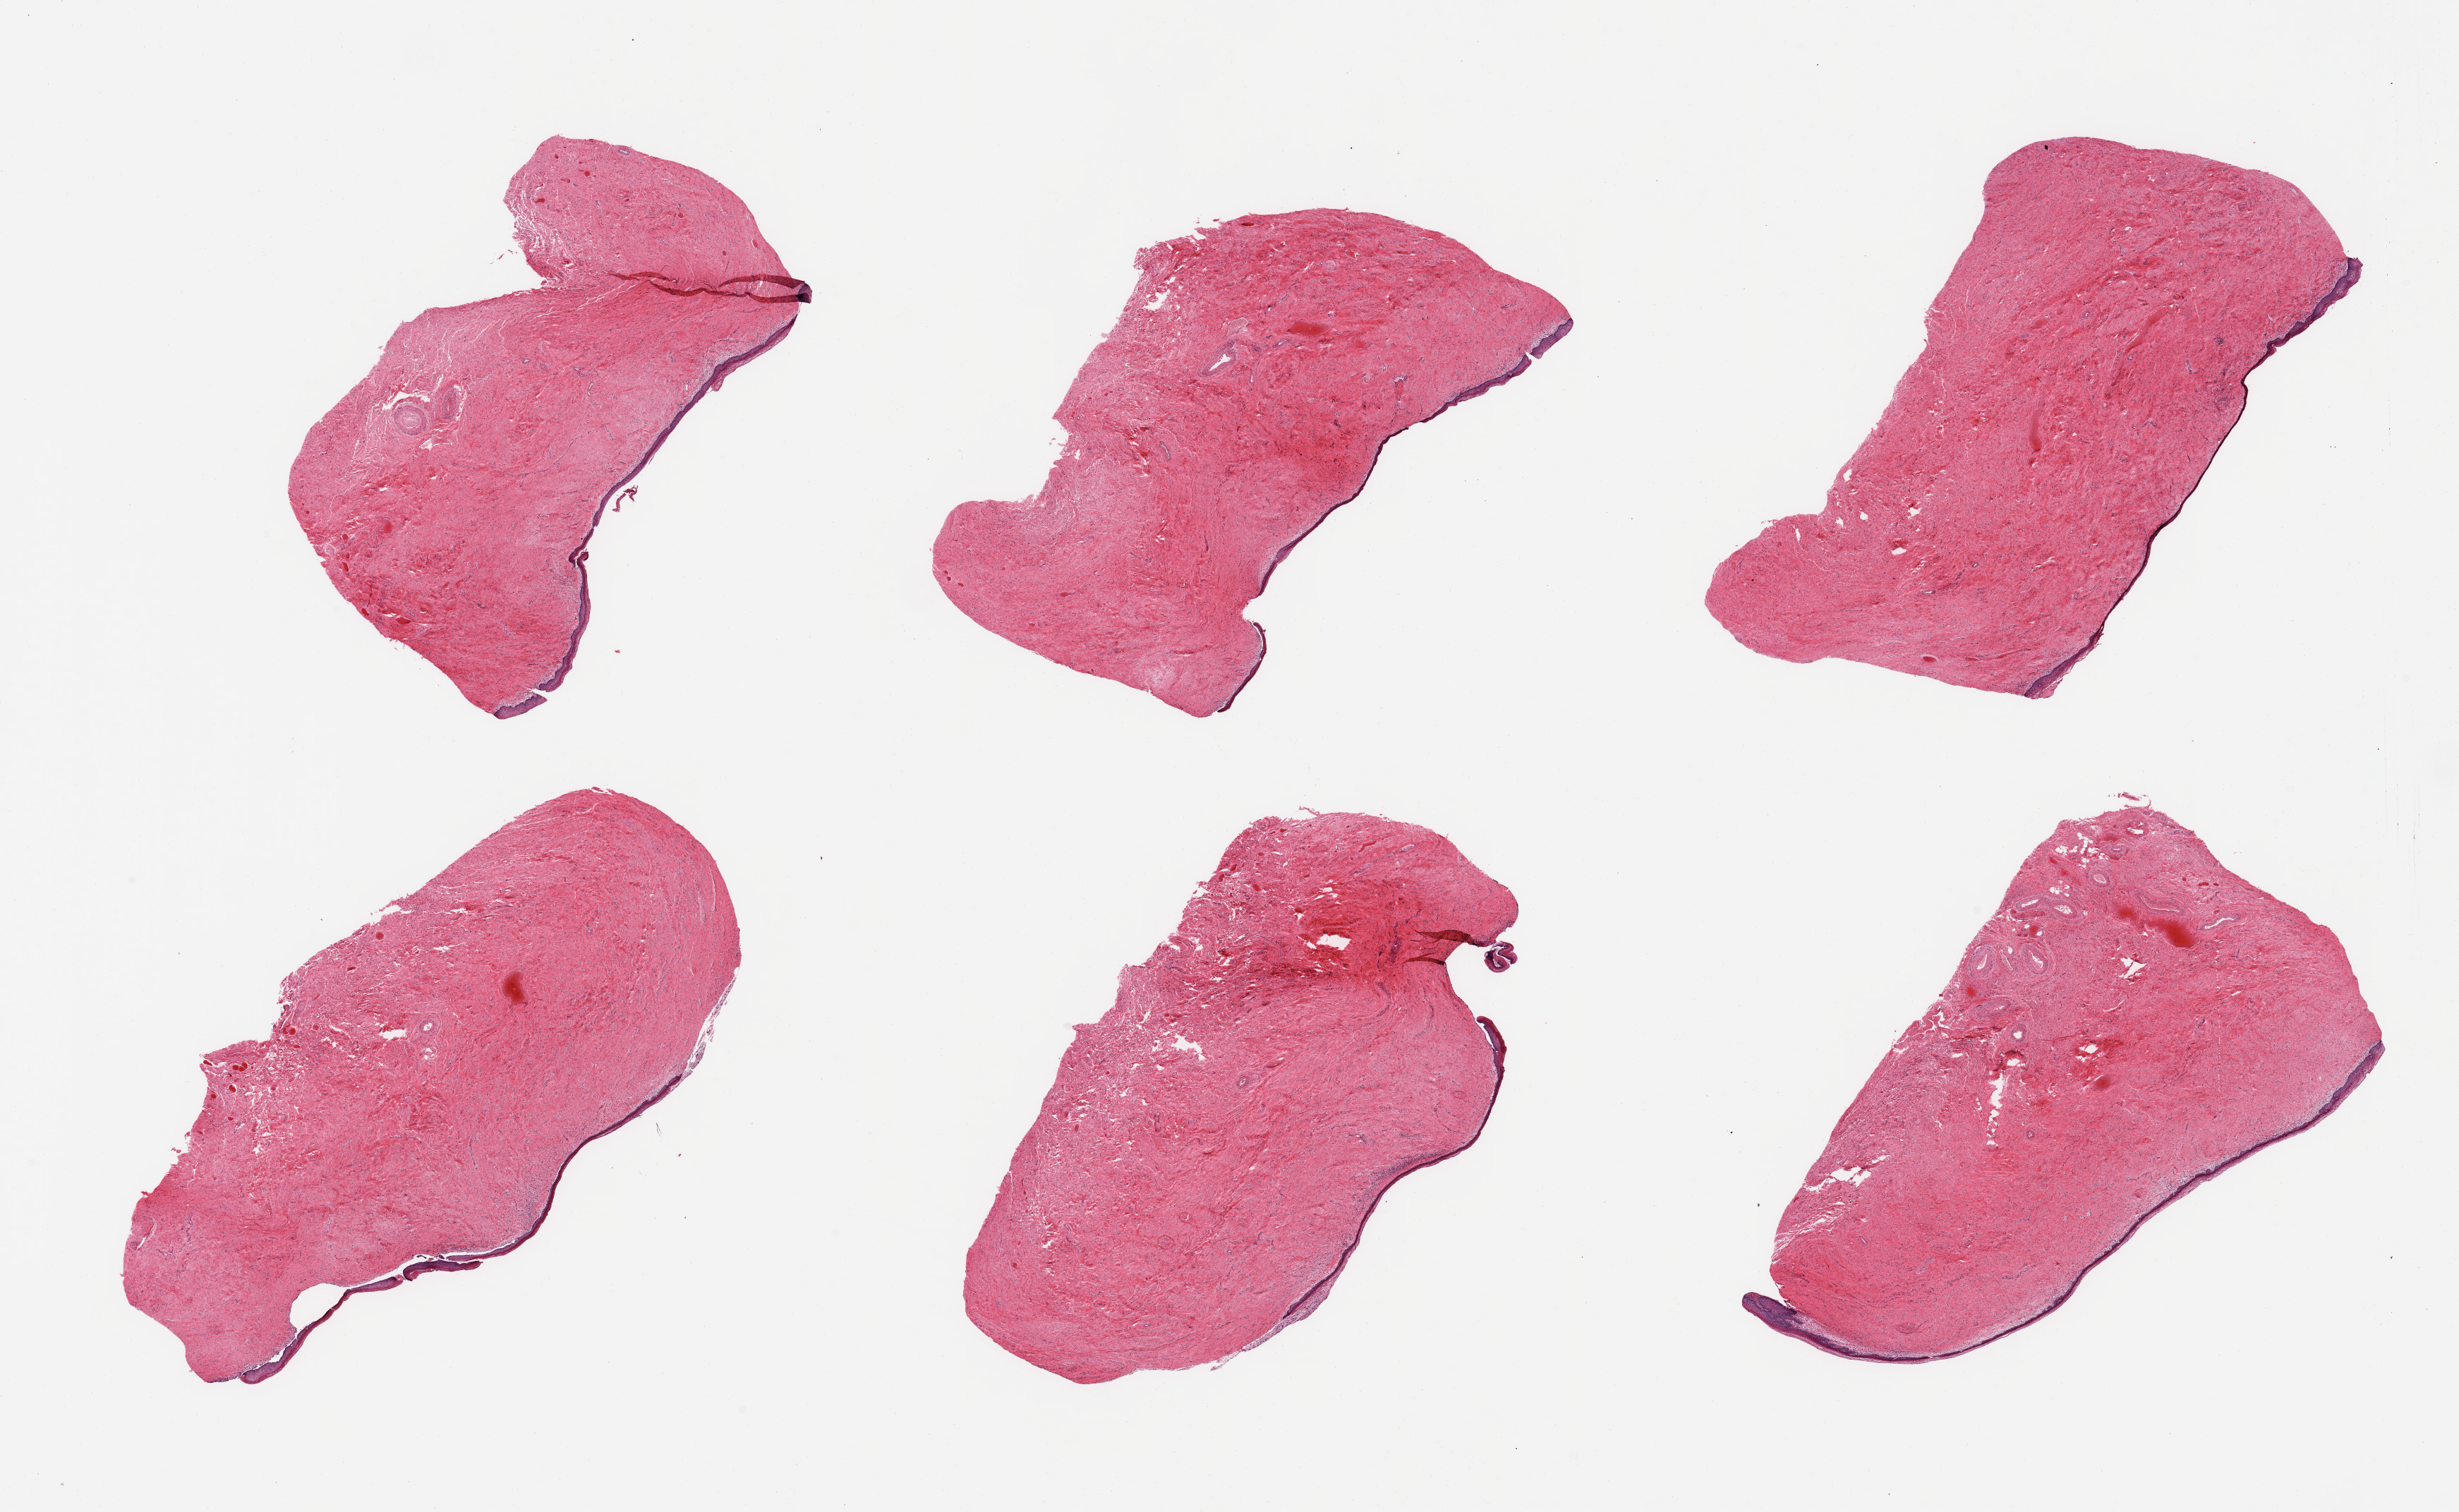
H&E whole-slide image, brightfield, a low-resolution overview of the entire scanned area, about 27.6 x 16.9 mm (slide scanned at 20x). PAXgene-fixed, paraffin-embedded tissue. Sampled site (target tissue): vagina. Donor tissue sample. Female donor.
Reviewer comment on this tissue sample: 6 pieces; atrophic epithelium with focal inflammatory exudate.